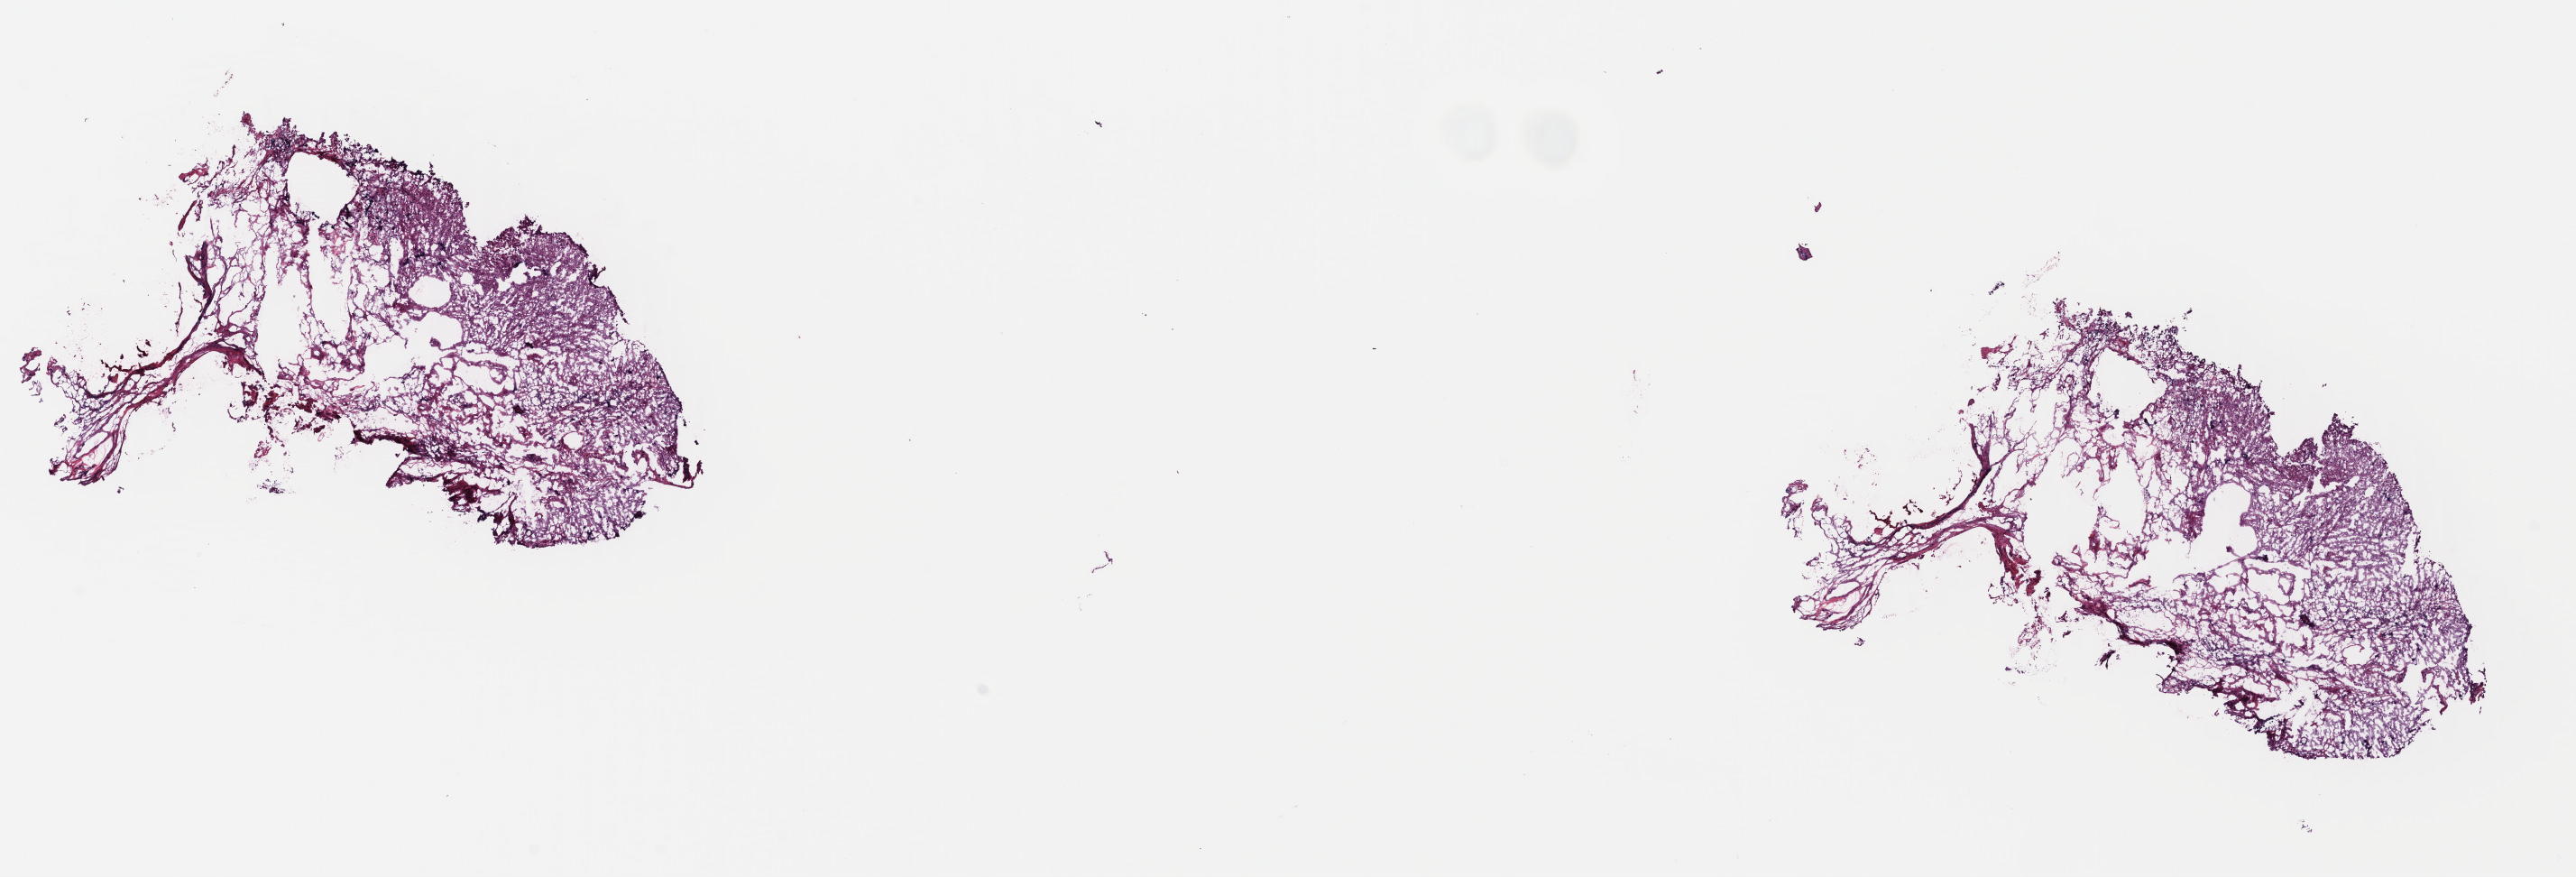
Digitized H&E-stained tissue section (whole slide) — whole scanned area (about 22.4 x 7.6 mm, acquisition: 40x scan) shown as a low-resolution overview, frozen section from the top of the tissue portion, sample: primary tumour, brain. Female, age 71 years at initial diagnosis. Histologic grade: G3 (poorly differentiated). Composition of this section per pathologist review: tumour cells 30%, tumour nuclei 70%, normal cells 10%, stromal cells 60%, necrosis 0%. Infiltration values recorded for this section: lymphocyte infiltration 0%, monocyte infiltration 0%, neutrophil infiltration 0%.
• histologic diagnosis: Oligodendroglioma, anaplastic (cerebrum)